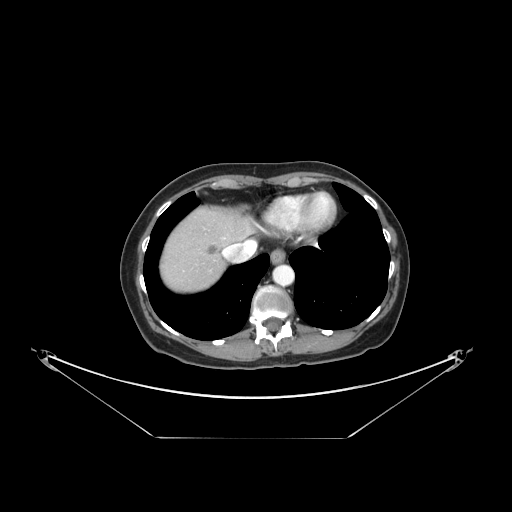
Contrast-enhanced abdominal CT, one axial slice; slice 132 of 148 in the series (ordered by position); 120 kVp; intravenous contrast given; soft-tissue window (W 400 / L 40 HU); 2.5 mm slice thickness; 512 × 512 image matrix. Female patient, age 73 years. Case-level facts recorded for this patient, not image findings: diagnosis: colorectal cancer liver metastases, imaged before liver resection; multiple liver metastases: no; largest metastasis: 1 cm; chemotherapy before resection: yes.
Annotated regions visible in this slice (outlined manually by an expert reader):
- liver: bounding box [x1, y1, x2, y2] px = [160, 209, 250, 291]
- planned liver remnant (the part of the liver to remain after resection): [190, 209, 251, 243]
- liver metastasis: [206, 245, 219, 257]